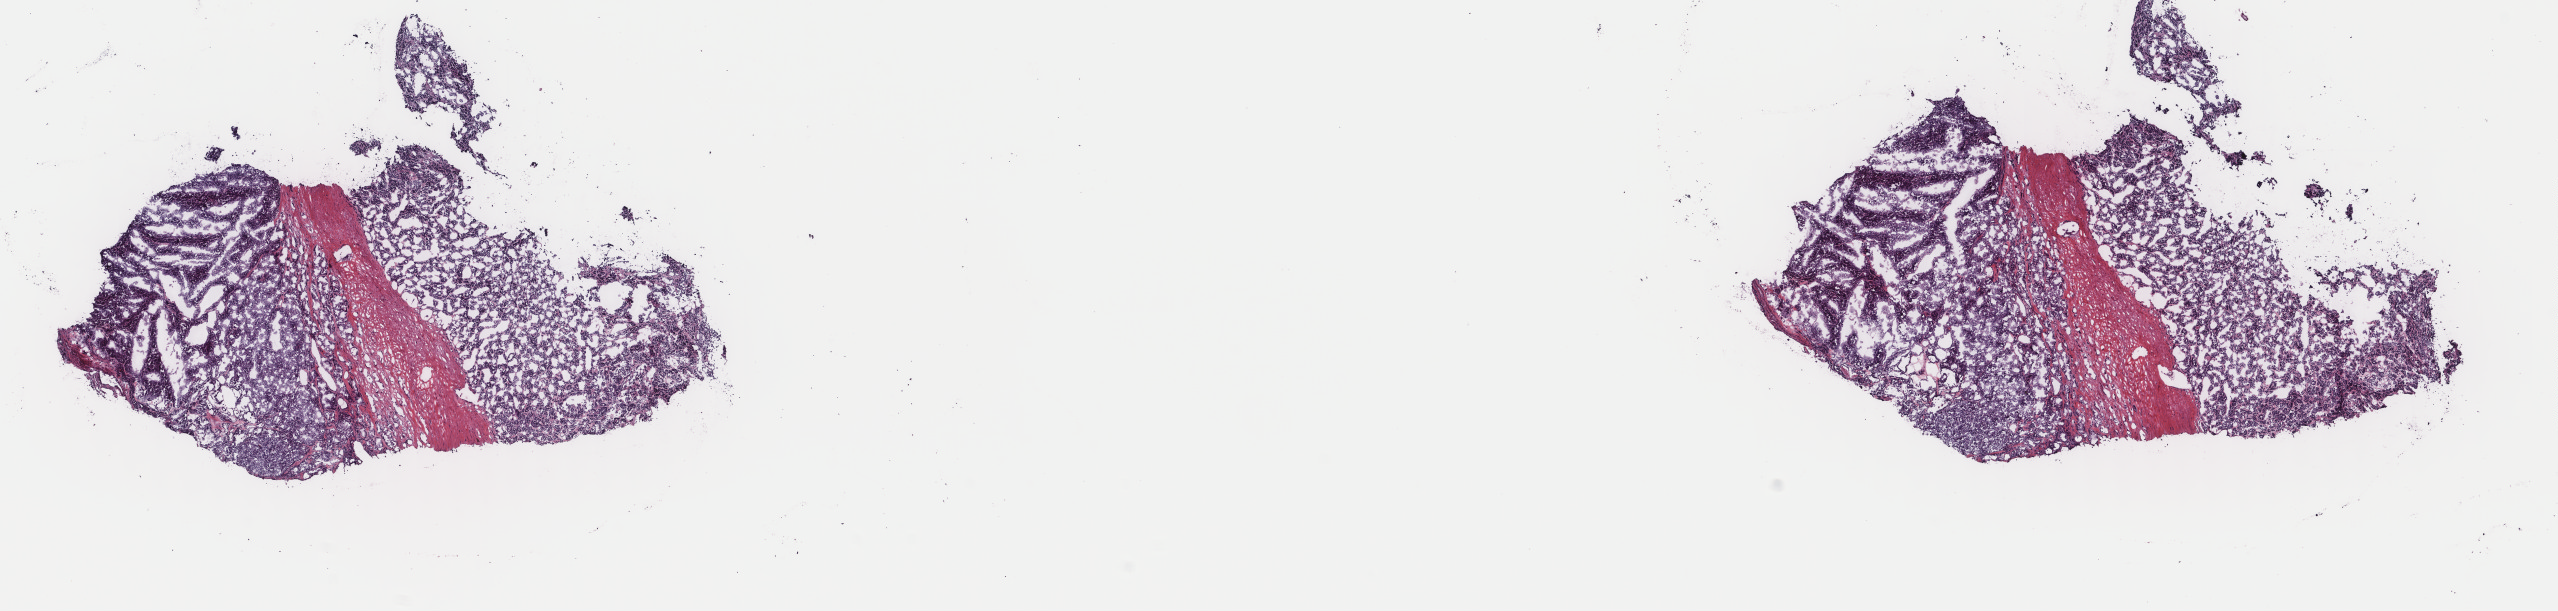
Digitized H&E tissue section (whole slide), low-resolution overview of the scanned area, about 20.3 x 4.8 mm, frozen section, sample: primary tumour, thyroid. Female, age 47 years at initial diagnosis. Pathologist review of this section (percent, as recorded): tumour cells 85%, tumour nuclei 100%.
Histologic diagnosis: Papillary carcinoma, follicular variant.